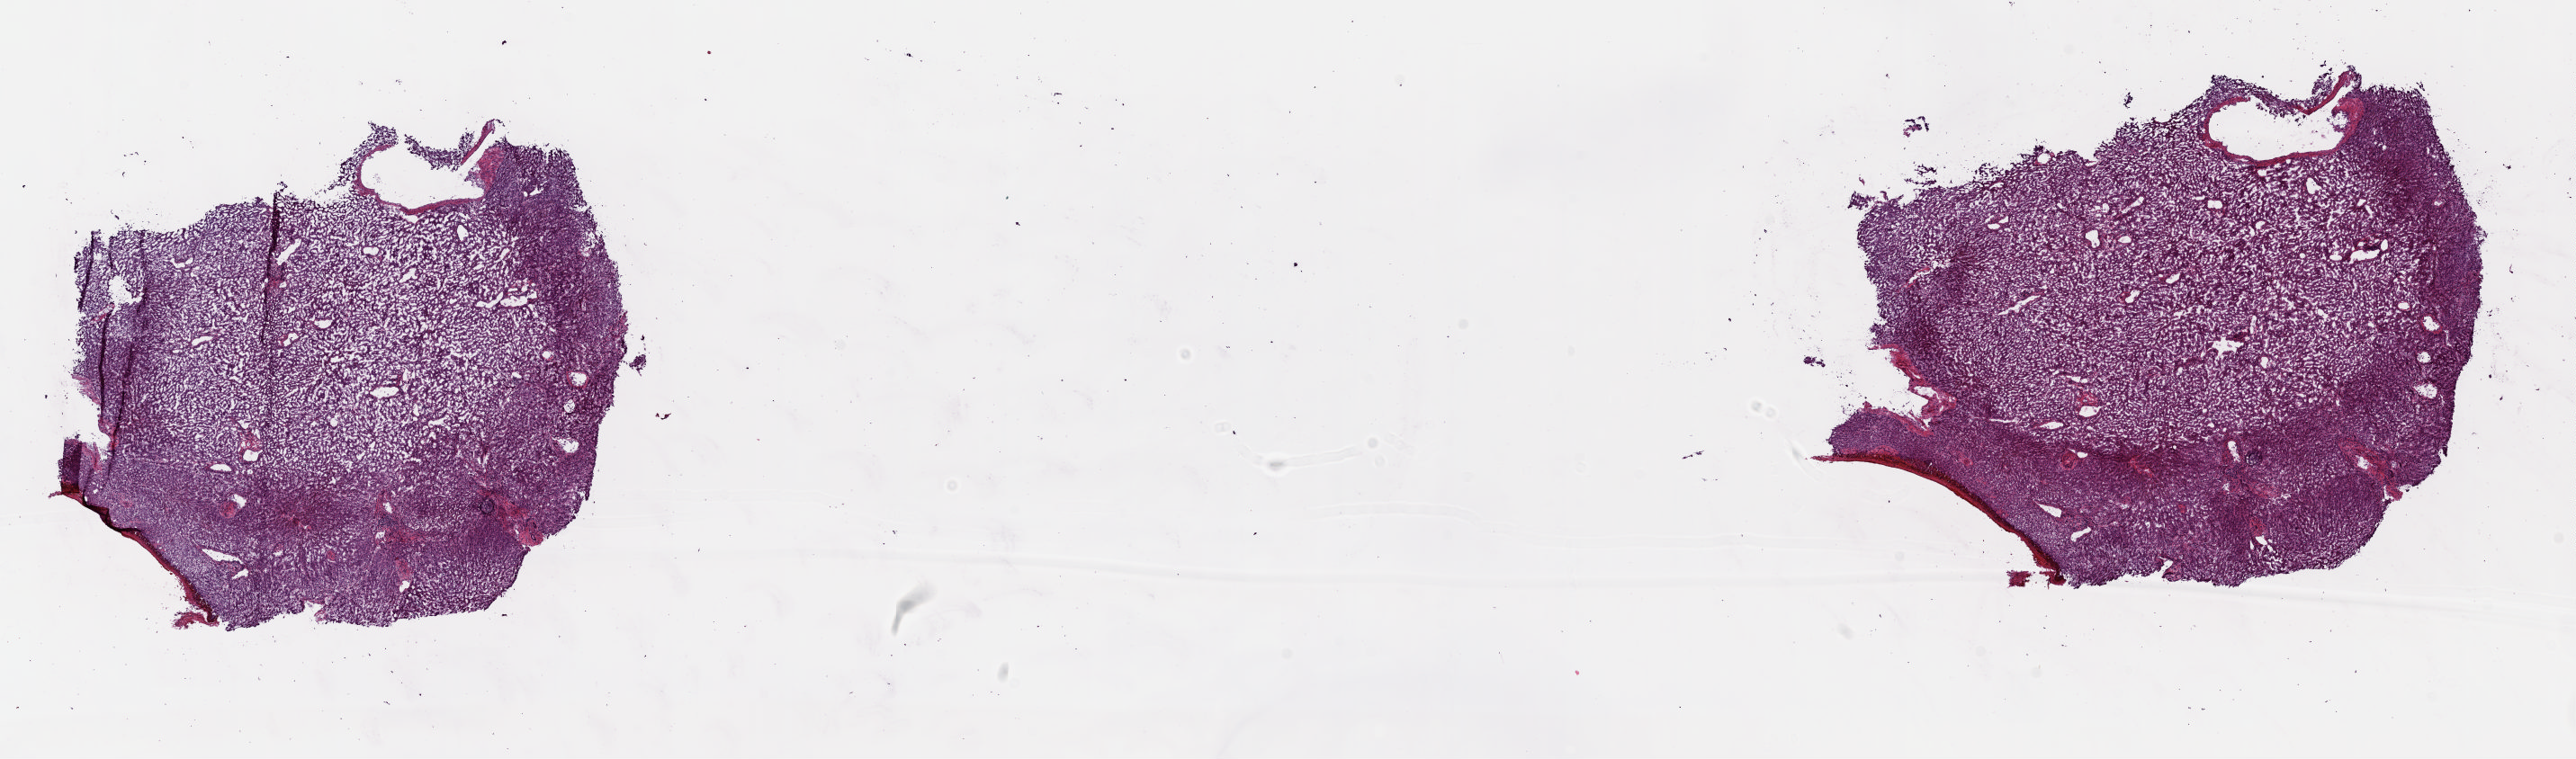
Whole-slide histology image, H&E-stained — low-resolution overview of the scanned area, about 22.7 x 6.7 mm (from a 20x scan); frozen section; liver, solid tissue normal (non-tumour tissue) sample. Female, age 79 years at initial diagnosis. Composition of this section per pathologist review: tumour cells 0%, tumour nuclei 0%, normal cells 100%, stromal cells 0%, necrosis 0%. Infiltration values recorded for this section: lymphocyte infiltration 0%, monocyte infiltration 0%, neutrophil infiltration 0%.
This section: solid tissue normal (non-tumour) sample from the same patient. Patient diagnosis: Hepatocellular carcinoma, NOS.